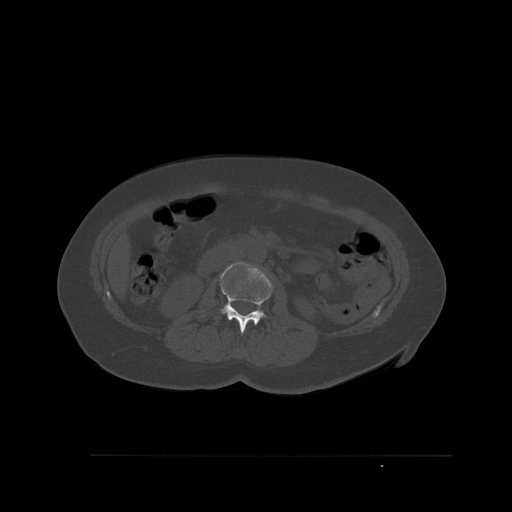
CT including the spine, one axial slice. Position 244 of 527 along the scan axis. Bone window (W 1800 / L 400 HU). 1.5 mm slice thickness. 512 × 512 image matrix. Patient: female, 73 years. Case-level facts recorded for this patient, not image findings: primary cancer: breast.
Structures marked on this image (semi-automatically segmented with operator editing):
- L1 vertebra: box from (x=241, y=352) to (x=243, y=354) px
- L2 vertebra: (x=202, y=261)–(x=270, y=334)